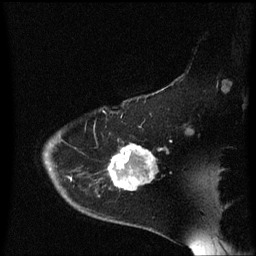
Breast MRI (dynamic contrast-enhanced), one sagittal slice. Position 47 of 60 along the scan axis. Dynamic contrast-enhanced series, image 2 of 3 at this slice position (ordered by acquisition). 1.5 T. TE 4.2 ms, TR 8.4 ms. 2 mm slice thickness. 256 × 256 image matrix, field of view 200 × 200 mm. Female patient, age 54 years. From the clinical record (not read from this slice): setting: breast cancer imaged before/during neoadjuvant chemotherapy; receptor status: HR-positive, HER2-negative.
Annotated regions visible in this slice (semi-automatically segmented with operator editing):
- analysis volume of interest (the breast-tissue region the enhancement analysis was run in; not a lesion): bounding box (x1, y1, x2, y2) in pixels: (110, 134, 156, 191)
- tumour enhancement mask (voxels above the 70 % enhancement threshold inside the analysis volume of interest): (110, 144, 156, 191)